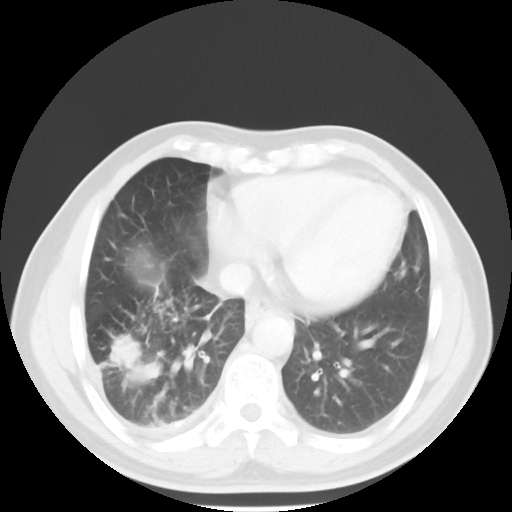
Chest CT, one axial slice. 120 kVp. Lung window (W 1500 / L -600 HU). 5 mm slice thickness. 512 × 512 image matrix. Male patient, age 56 years. Case-level facts recorded for this patient, not image findings: clinical TNM (as recorded): T2 N3 M1.
Outlined on this slice (bounding box drawn by a radiologist):
- lung tumour (recorded histology: adenocarcinoma): bounding box (x1, y1, x2, y2) in pixels: (107, 336, 159, 386)